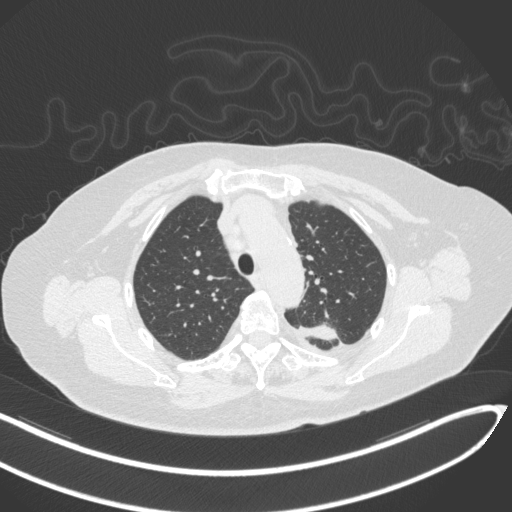
Chest CT, one axial slice; position 243 of 270 along the scan axis; reconstruction kernel B31f; 120 kVp; lung window (W 1500 / L -600 HU); 512 × 512 image matrix, field of view 400 × 400 mm. Female patient, age 76 years. From the clinical record (not read from this slice): clinical TNM (as recorded): T1c N0 M0.
Structures marked on this image (rectangle marked by the reading radiologist):
- lung tumour (recorded histology: adenocarcinoma): bounding box [x1, y1, x2, y2] px = [301, 318, 340, 342]